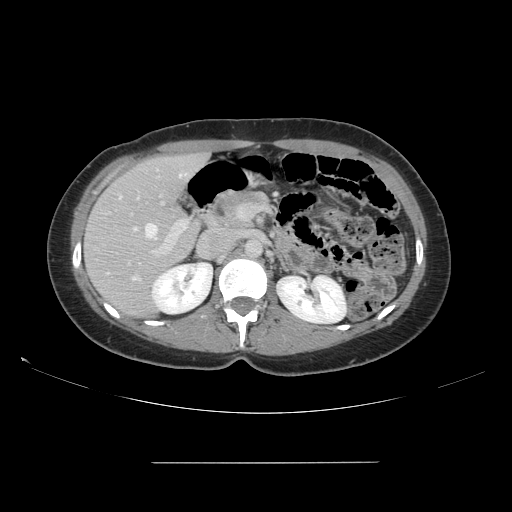
Contrast-enhanced abdominal CT, one axial slice; position 86 of 151 along the scan axis; 120 kVp; intravenous contrast given; soft-tissue window (W 400 / L 40 HU); 512 × 512 image matrix. Female patient, age 46 years. From the clinical record (not read from this slice): diagnosis: colorectal cancer liver metastases, imaged before liver resection; multiple liver metastases: yes; largest metastasis: 3 cm.
Structures marked on this image (outlined manually by an expert reader):
- hepatic veins: bounding box (x1, y1, x2, y2) in pixels: (119, 173, 187, 279)
- liver: (85, 155, 207, 318)
- planned liver remnant (the part of the liver to remain after resection): (94, 154, 201, 310)
- portal vein (with intrahepatic branches): (130, 190, 246, 257)